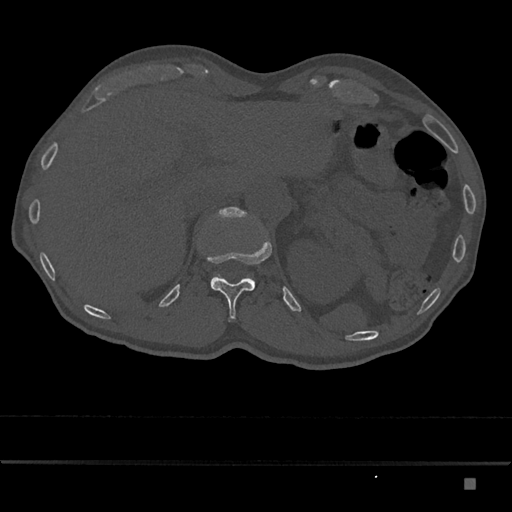
CT including the spine, one axial slice; position 598 of 797 along the scan axis; bone window (W 1800 / L 400 HU); 512 × 512 image matrix, field of view 390 × 390 mm. Male patient, age 72 years. Case-level facts recorded for this patient, not image findings: primary cancer: prostate.
Annotated regions visible in this slice (semi-automatic segmentation, software-assisted and operator-edited):
- L1 vertebra: bounding box <210,207,255,288> (left, top, right, bottom; pixels)
- T12 vertebra: <208,241,272,321>